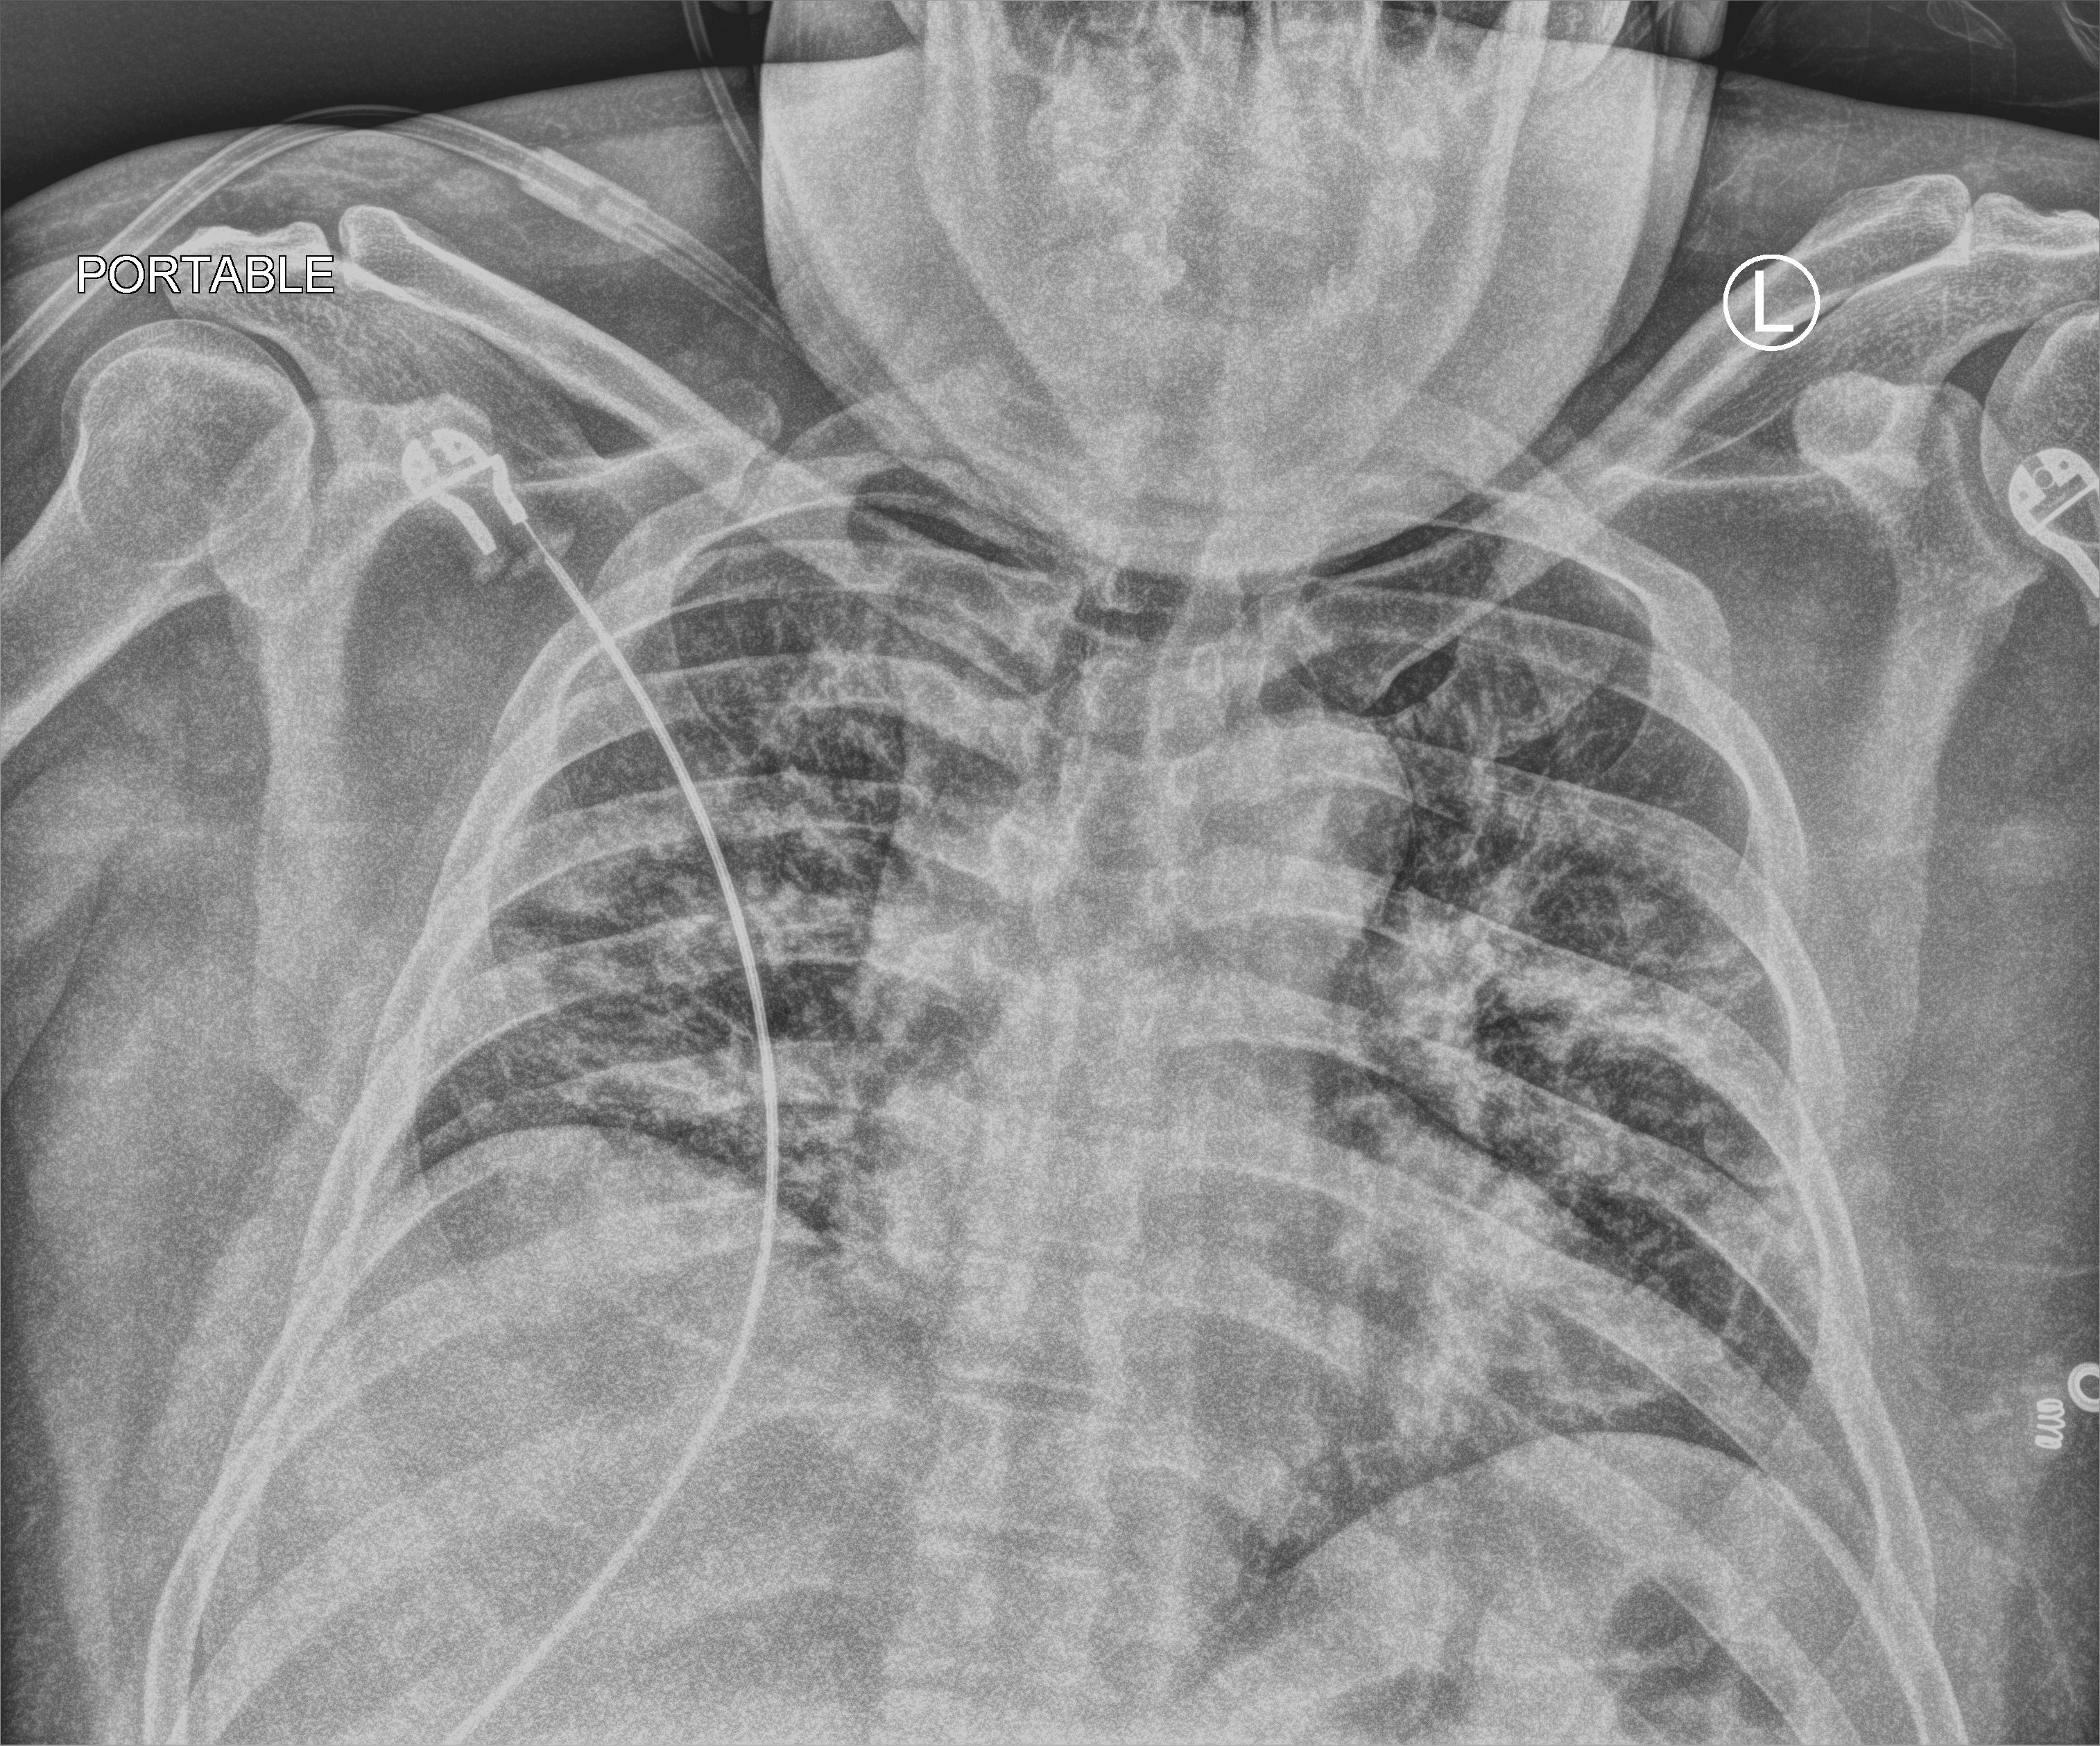
Chest X-ray (portable); anteroposterior (AP) projection. Patient hospitalised with COVID-19; male, aged 18–59 years.
From the hospital-stay record, not from the radiograph (when in the stay this image was taken is not recorded): hypertension (admission record): yes; mechanically ventilated during this hospital stay: no; smoking status (admission record): never.